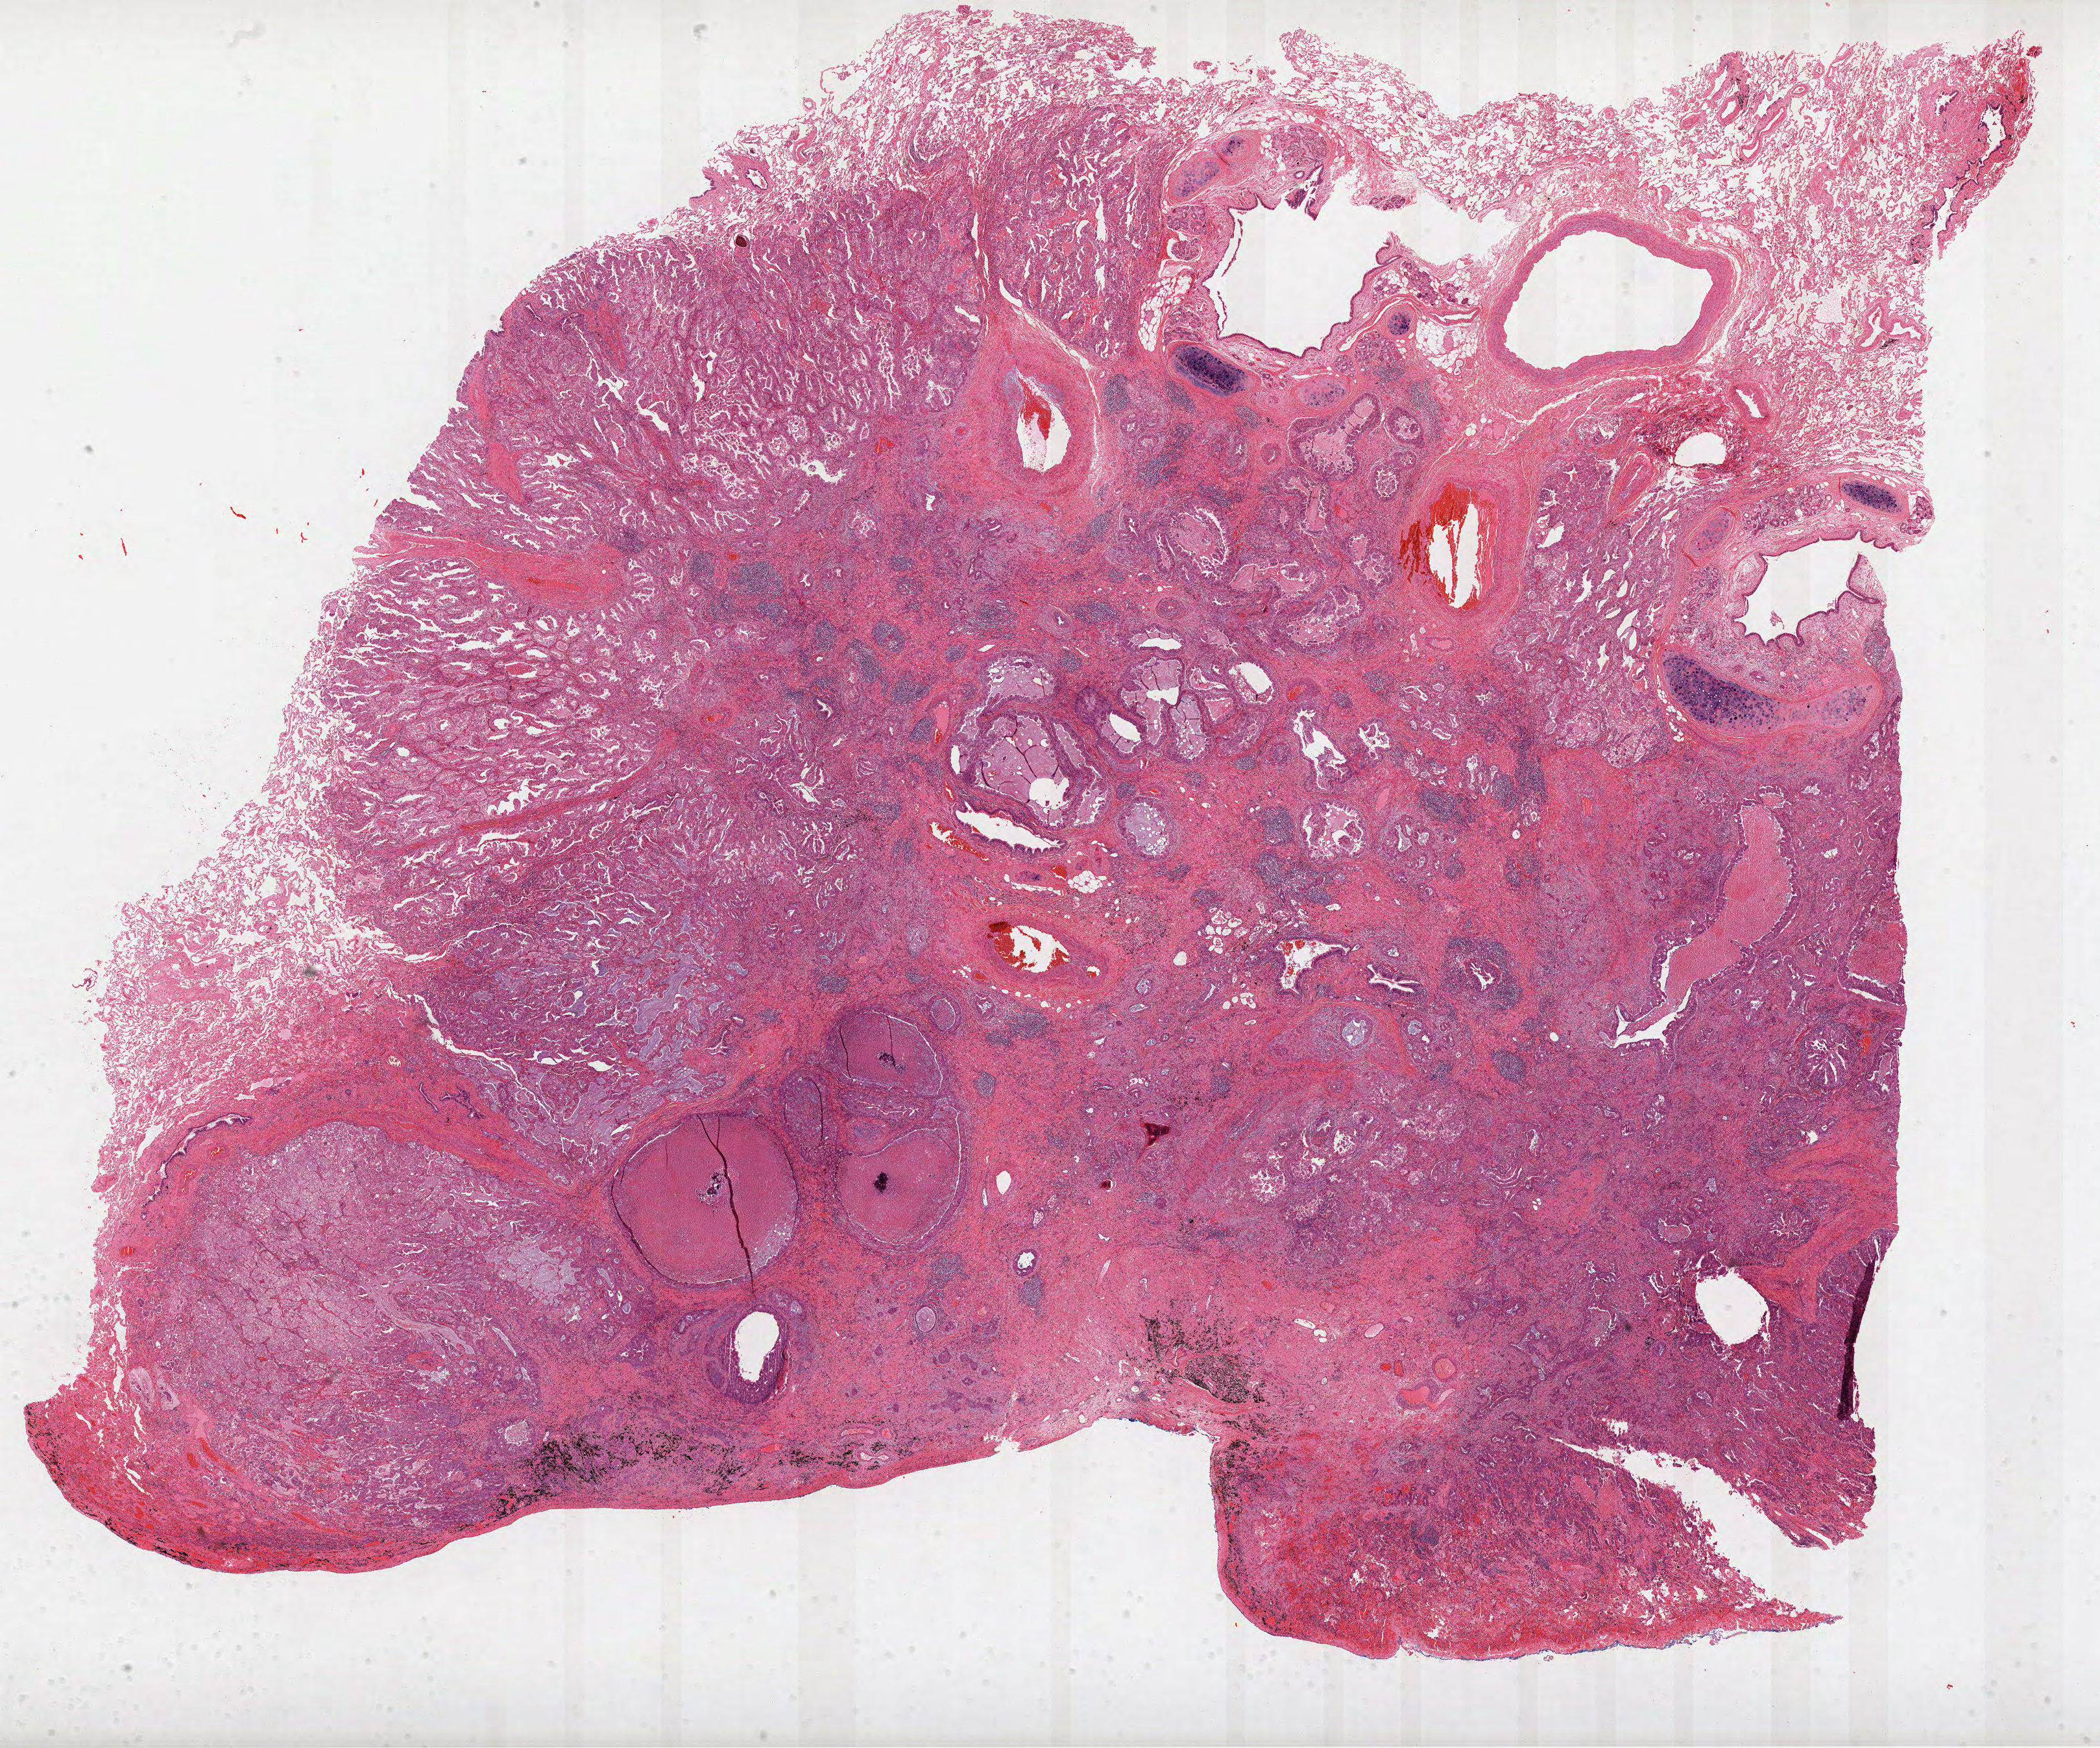
Digitized H&E tissue section (whole slide) — shown as a low-resolution overview of the whole scanned area (about 26.1 x 21.7 mm); FFPE section; sample: primary tumour, lung. Male patient; age at initial diagnosis 77 years.
Laterality: left. Histologic diagnosis: Adenocarcinoma, NOS. AJCC pathologic stage: IB.